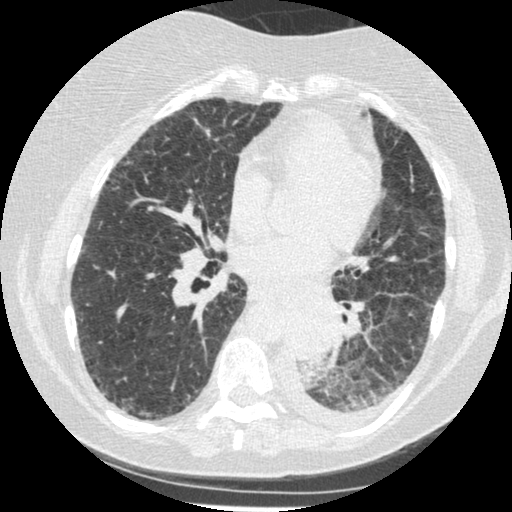
Low-dose screening chest CT, one axial slice; slice 105 of 341 in the series (ordered by position); lung window (W 1500 / L -600 HU); 512 × 512 image matrix, field of view 310 × 310 mm.
Outlined on this slice (outlined manually by an expert reader):
- lesion 1 (tumor, lower lobe of left lung): bounding box <285,304,339,364> (left, top, right, bottom; pixels)